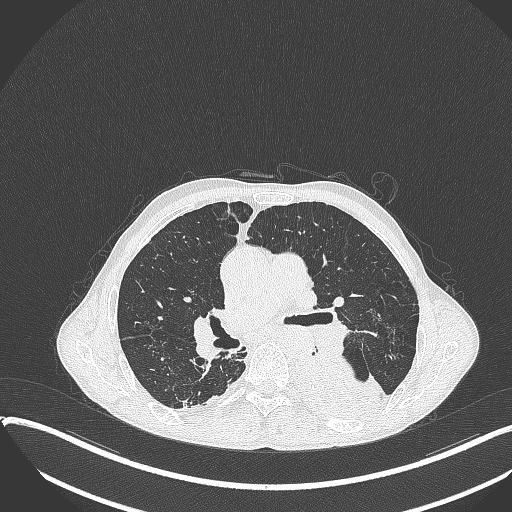
Chest CT, one axial slice. Slice 221 of 401 in the series (ordered by position). Lung window (W 1500 / L -600 HU). 1 mm slice thickness. 512 × 512 image matrix, field of view 400 × 400 mm. Patient: male, 57 years. Case-level facts recorded for this patient, not image findings: clinical TNM (as recorded): T4 N0 M0.
Annotated regions visible in this slice (rectangle marked by the reading radiologist):
- lung tumour (recorded histology: squamous cell carcinoma): box from (x=289, y=352) to (x=394, y=427) px